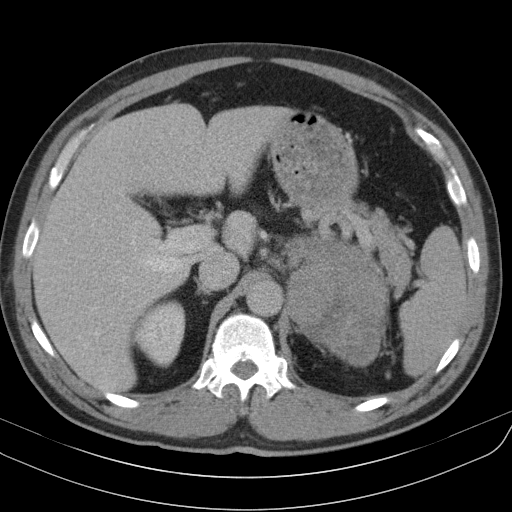
Contrast-enhanced abdominal CT, one axial slice; slice 71 of 91 in the series (ordered by position); reconstruction kernel B31s; soft-tissue window (W 400 / L 40 HU); 5 mm slice thickness; 512 × 512 image matrix, field of view 370 × 370 mm. Patient: male, 51 years. From the clinical record (not read from this slice): diagnosis: adrenocortical carcinoma; tumour side: left adrenal; tumour size at pathology: 18 cm; Ki-67 index: 40 %; stage (as recorded): 3.
Structures marked on this image (semi-automatically segmented with operator editing):
- mass: box from (x=288, y=237) to (x=388, y=365) px